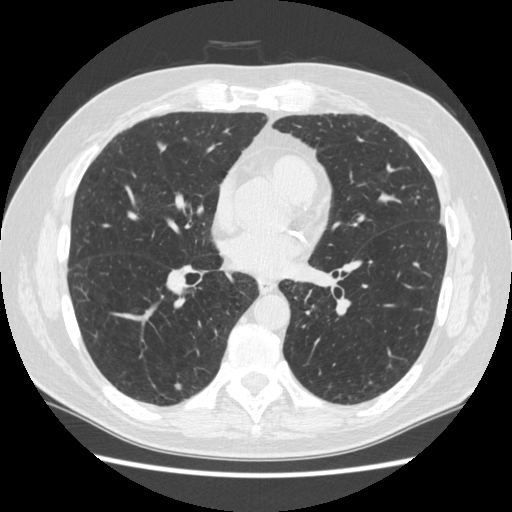
Low-dose screening chest CT, one axial slice; slice 123 of 267 in the series (ordered by position); reconstruction kernel STANDARD; 120 kVp; lung window (W 1500 / L -600 HU); 512 × 512 image matrix.
Outlined on this slice (manually delineated by an expert):
- lesion 3 (nodule, lower lobe of right lung): bounding box [x1, y1, x2, y2] px = [175, 383, 182, 390]